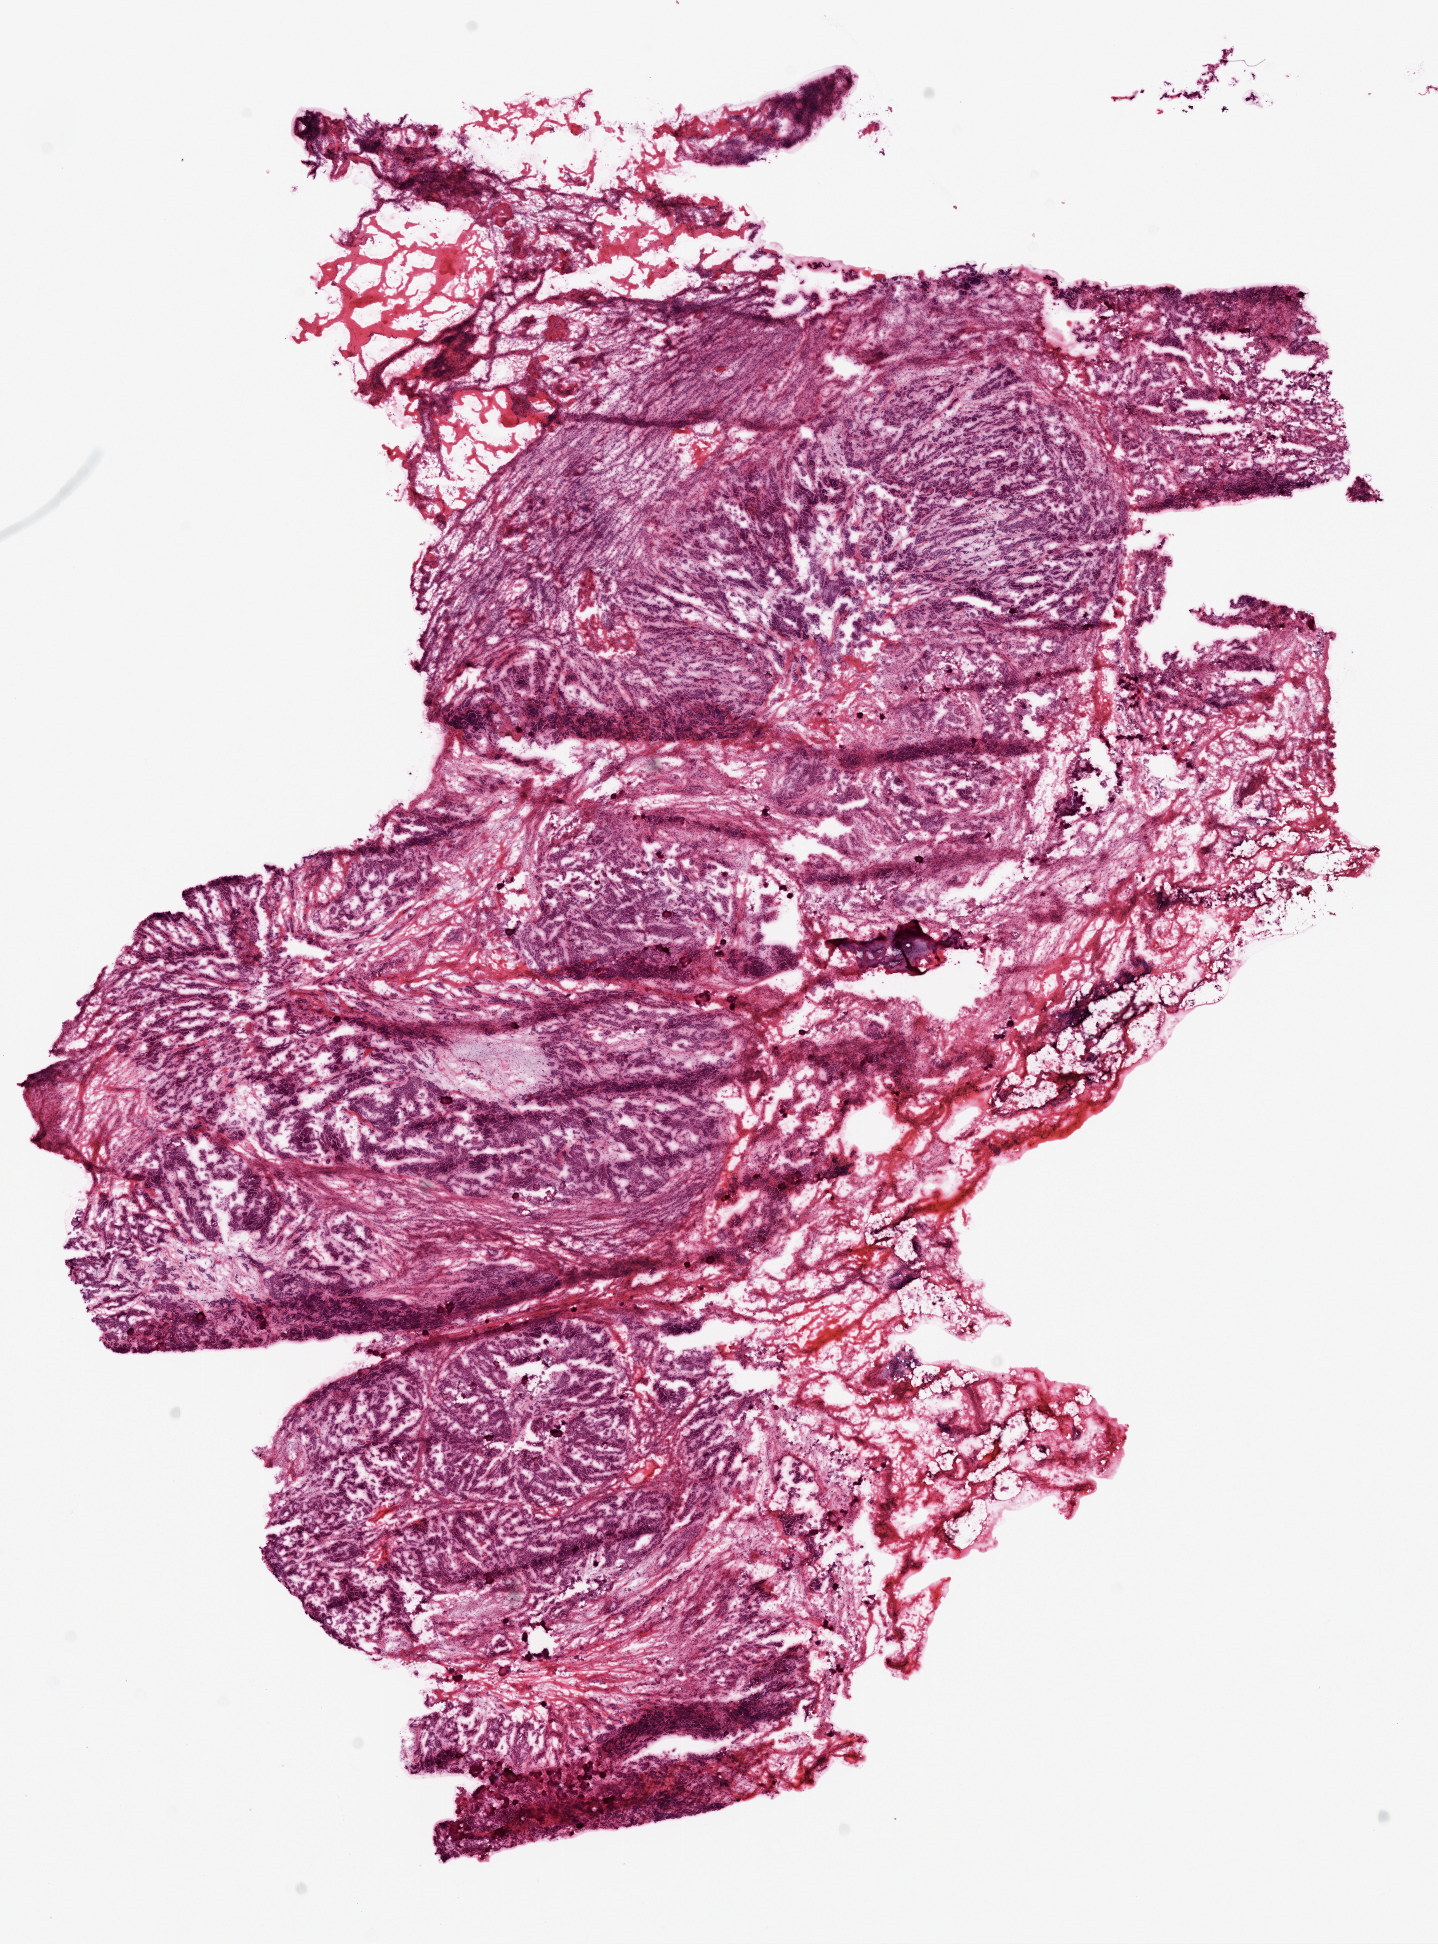
Whole-slide histology image, H&E, shown as a low-resolution overview of the whole scanned area (about 11.6 x 15.7 mm, slide scanned at 20x). Frozen section from the top of the tissue portion. Primary tumour sample from the ovary. Female patient; age at initial diagnosis 38 years. Histologic grade: G3 (poorly differentiated). Pathologist review of this section (percent, as recorded): tumour cells 90%, tumour nuclei 95%, stromal cells 5%, necrosis 5%.
Laterality: bilateral. Pathologic diagnosis: Serous cystadenocarcinoma, NOS. FIGO stage: IIIC.